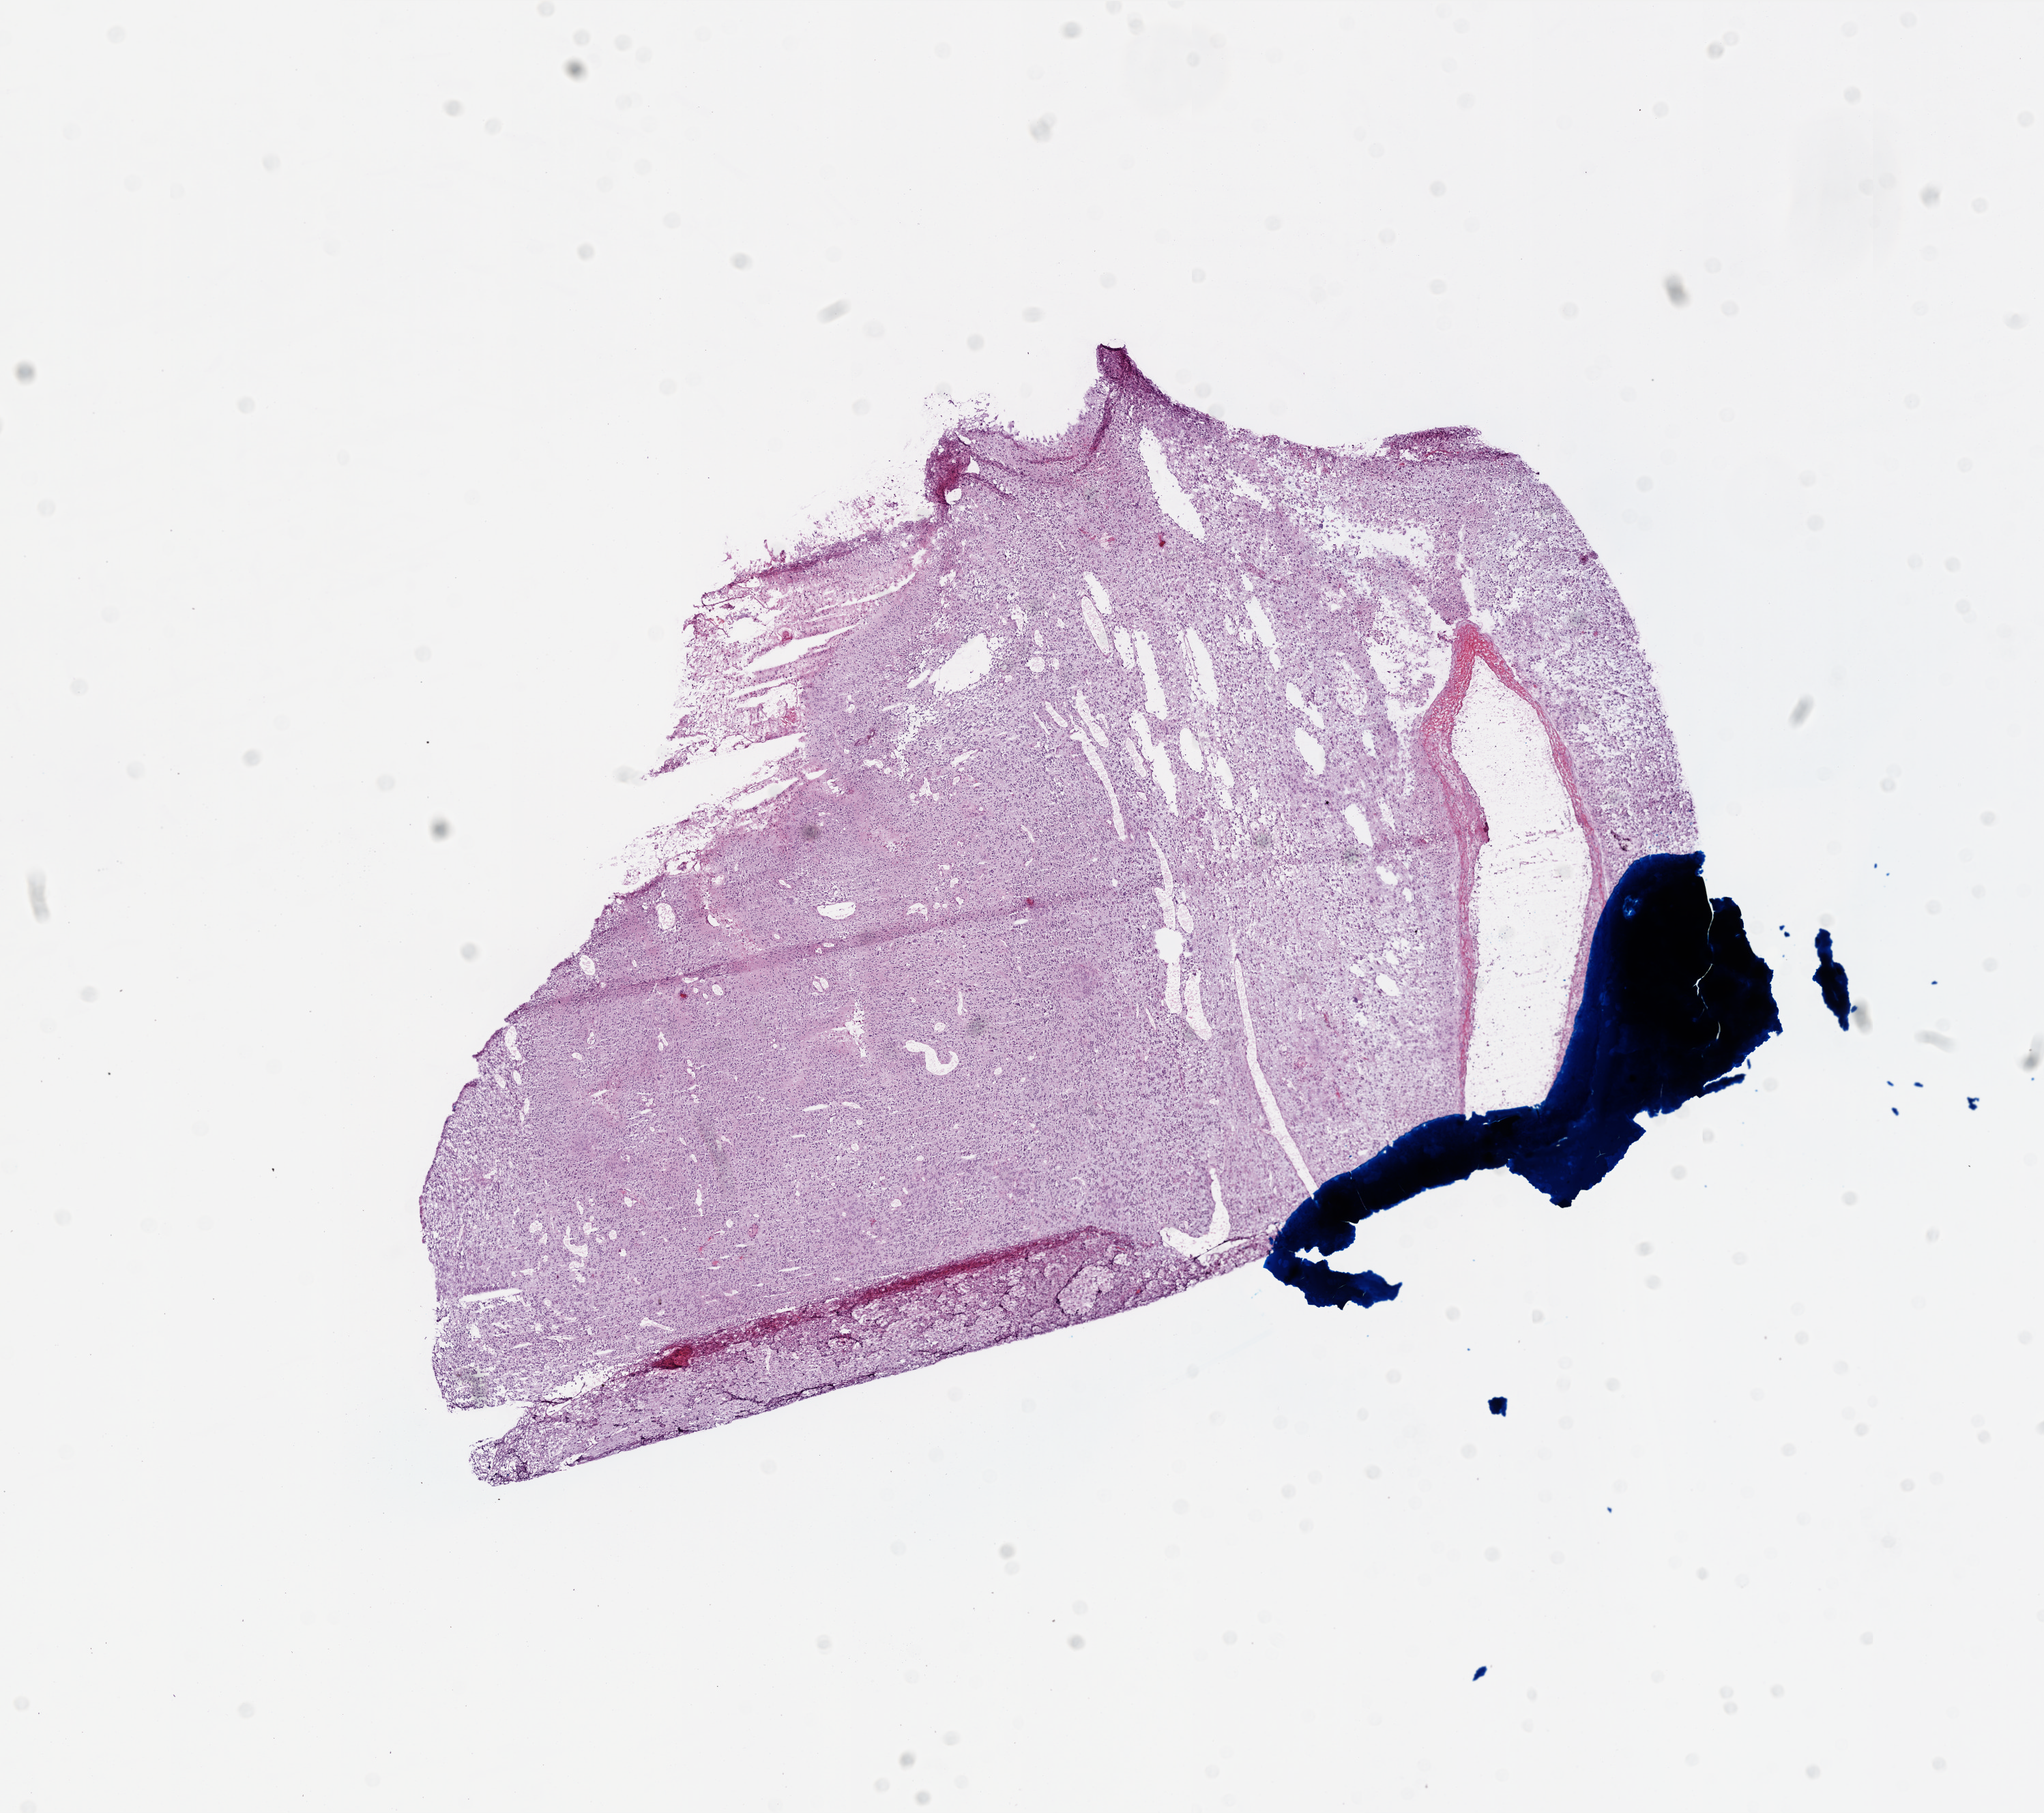
Whole-slide histology image, H&E, low-resolution overview of the scanned area, about 12.0 x 10.6 mm (acquisition: 20x scan); frozen section from the top of the tissue portion; brain, primary tumour sample. Male, age 74 years at initial diagnosis. Composition of this section per pathologist review: tumour cells 90%, tumour nuclei 100%, normal cells 0%, stromal cells 0%, necrosis 10%.
Pathologic diagnosis: Glioblastoma.